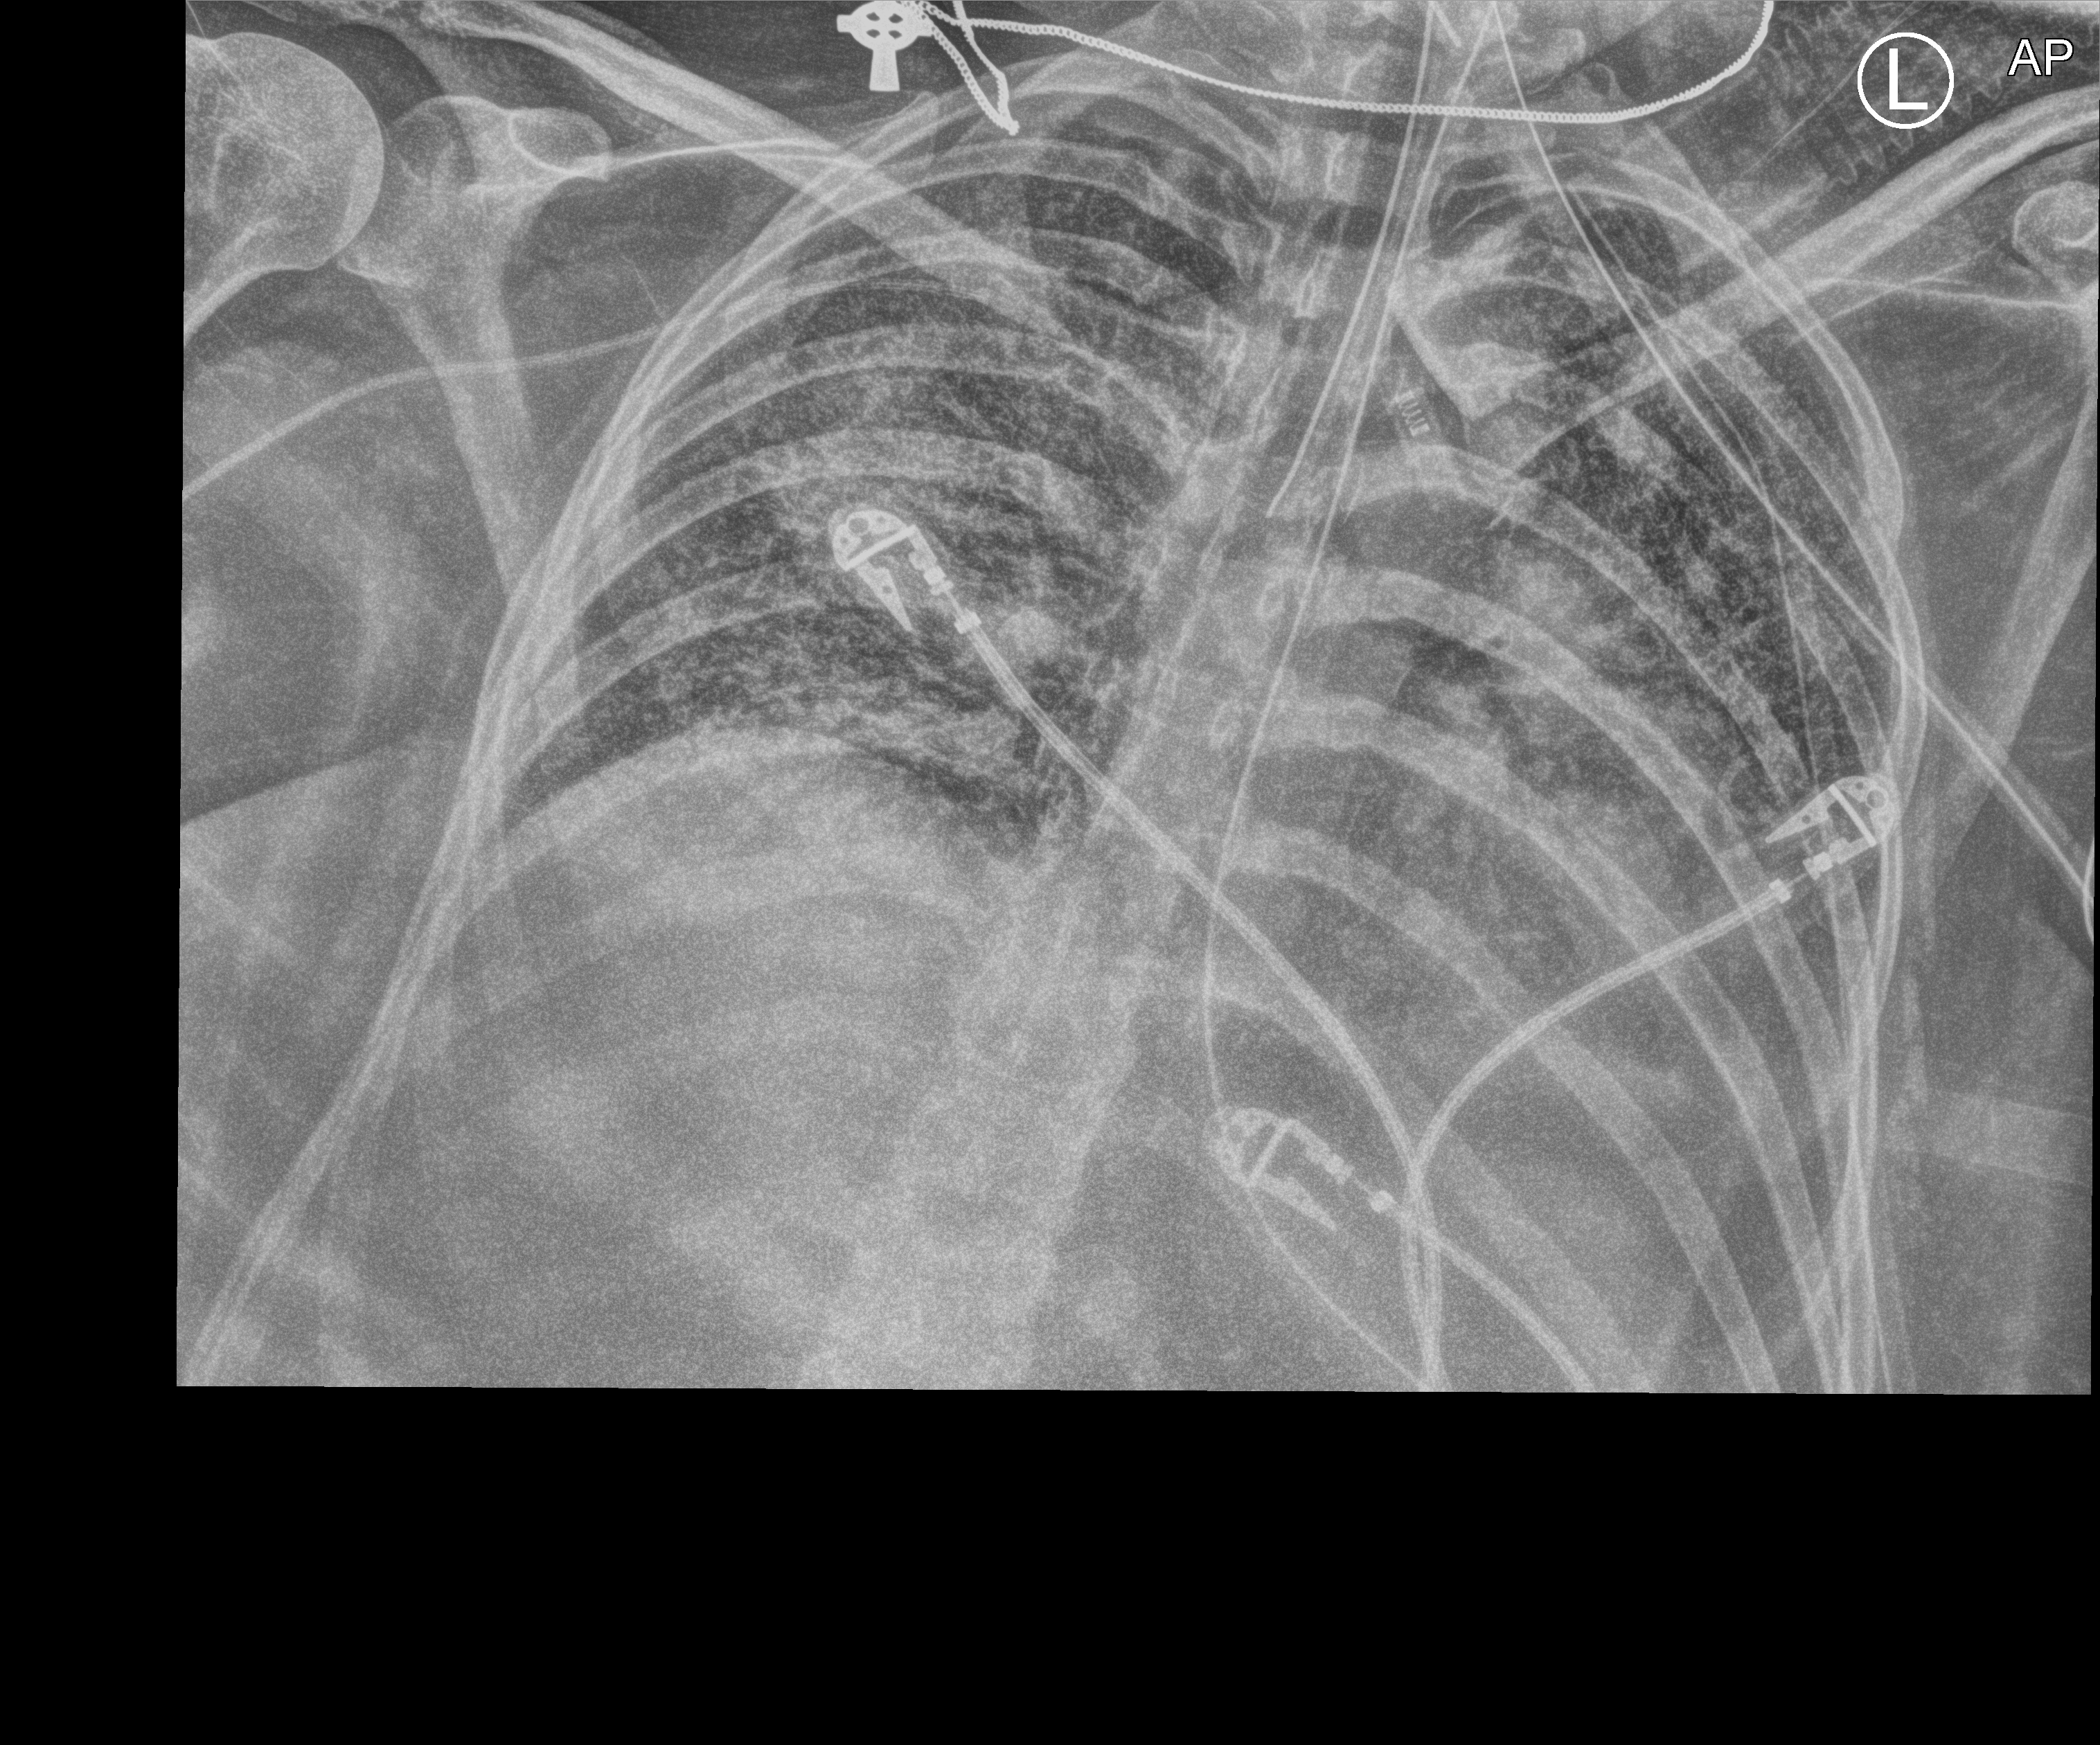
Chest X-ray (portable), anteroposterior (AP) projection. Patient hospitalised with COVID-19; female, aged 18–59 years.
Hospital-stay facts (about this admission, not read from this image; timing relative to this image not recorded):
- mechanically ventilated during this hospital stay: yes
- diabetes (admission record): no
- other chronic lung disease (admission record): yes